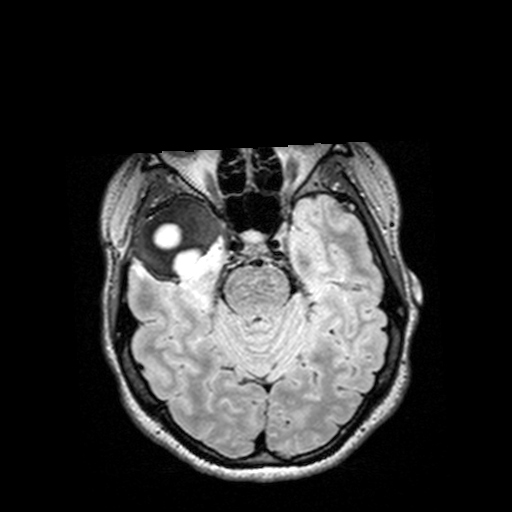
Brain MRI from a brain-tumour surgery series, one axial slice; slice 97 of 144 in the series (ordered by position); T2 FLAIR; 1 mm slice thickness; 512 × 512 image matrix, field of view 250 × 250 mm. Case-level facts recorded for this patient, not image findings: histopathology: Astrocytoma; WHO grade: 3; IDH mutation: yes; tumour location: Right Insular Temporal.
Structures marked on this image (outlined manually by an expert reader):
- tumour: bounding box [x1, y1, x2, y2] px = [126, 196, 232, 284]